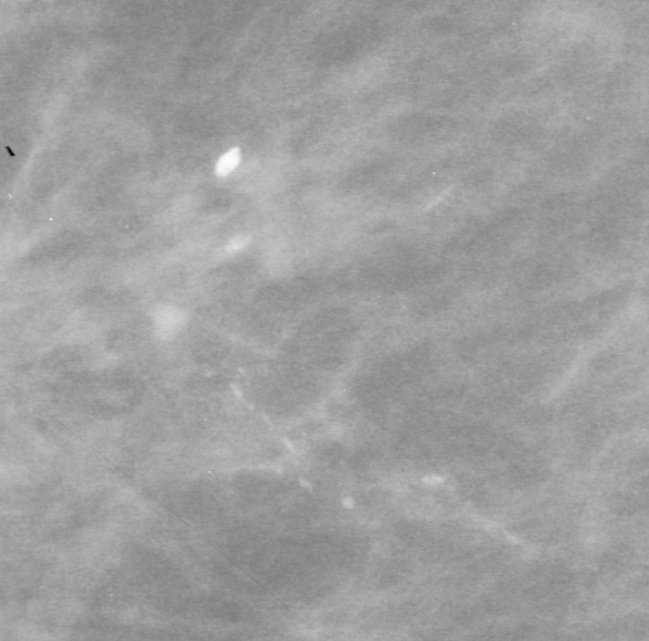
Cropped region of a digitized screen-film mammogram centred on a radiologist-marked abnormality, left breast, MLO view, BI-RADS breast density category 2 (scale 1–4).
Calcifications, morphology pleomorphic, distribution linear; BI-RADS assessment category 4; subtlety rating 4 on a 1 (subtle) to 5 (obvious) scale; pathology result (as recorded, not read from the image): malignant.